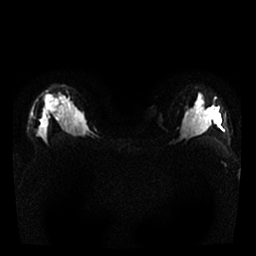
Breast MRI, one axial slice. Position 18 of 25 along the scan axis. Diffusion-weighted series; image 2 of 4 stored at this slice position (different b-values; order by instance number). 1.5 T. 4 mm slice thickness. 256 × 256 image matrix, field of view 320 × 320 mm. Female patient.
Structures marked on this image (outlined manually by an expert reader):
- tumour on diffusion-weighted imaging: box from (x=44, y=94) to (x=59, y=112) px